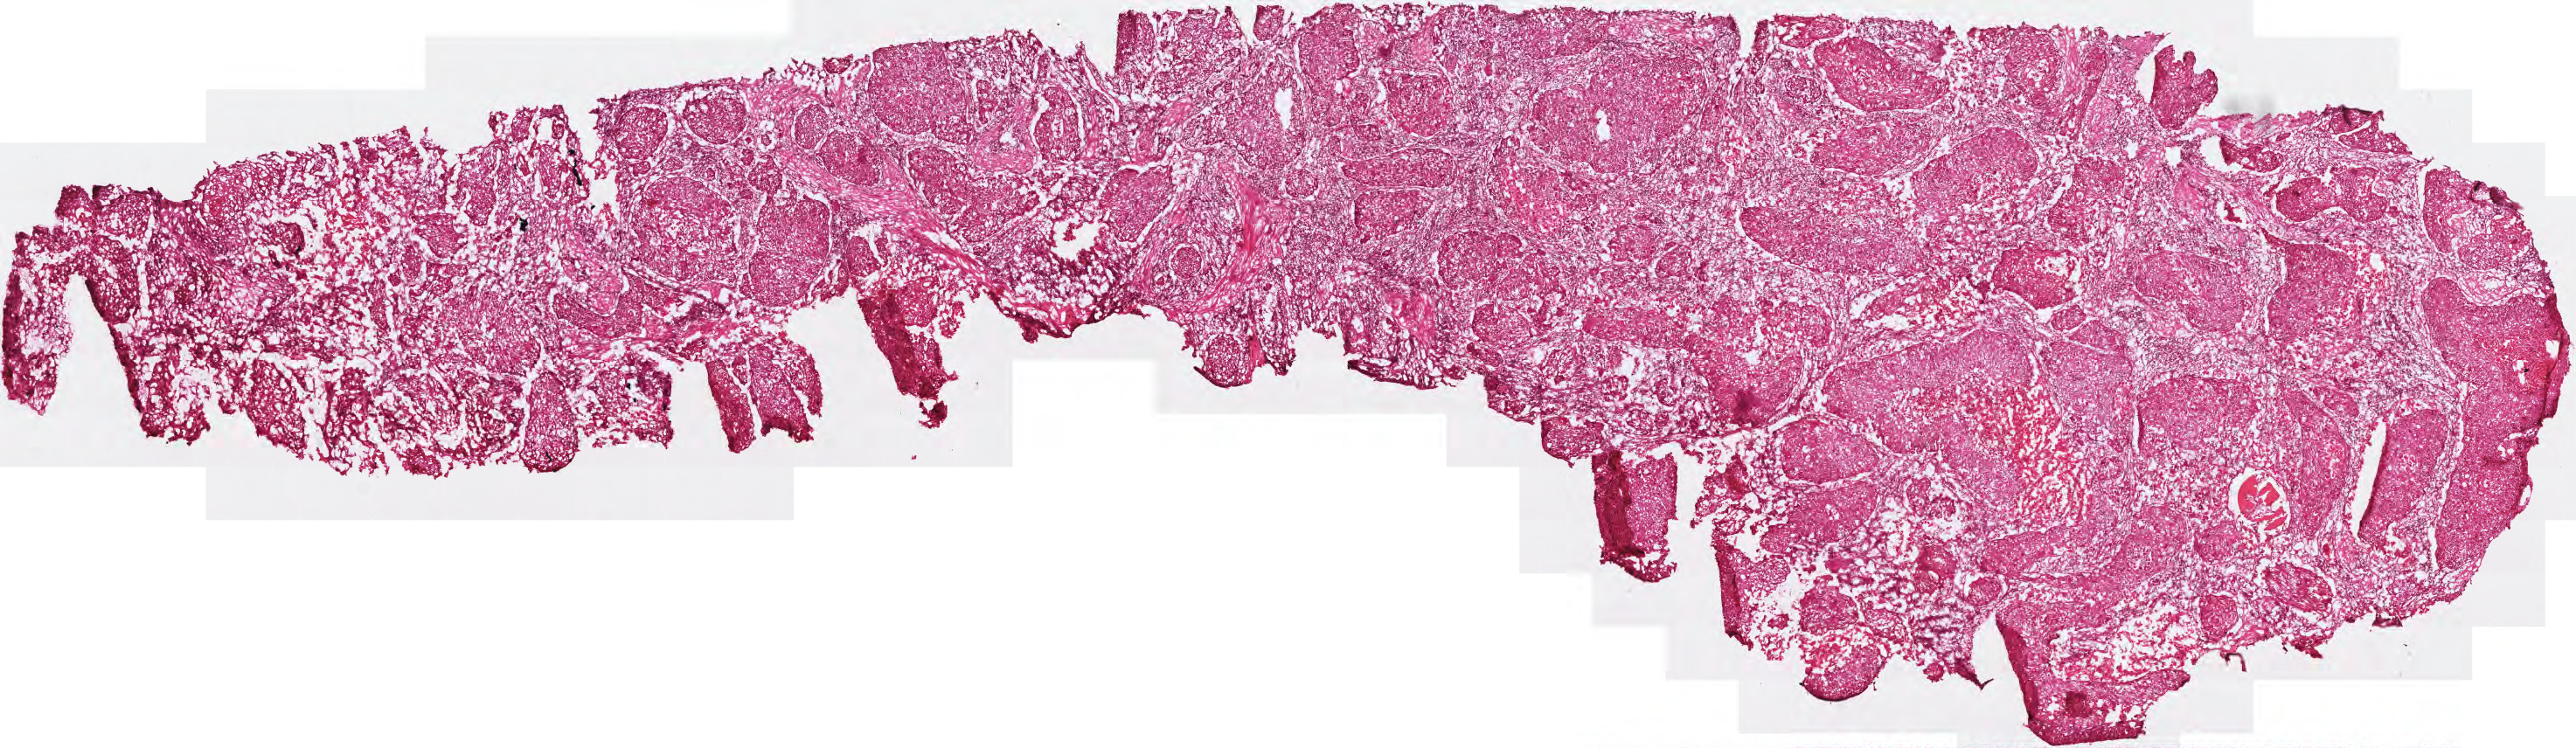
Whole-slide histology image, H&E, shown as a low-resolution overview of the whole scanned area (about 5.9 x 1.7 mm); frozen section; sample: primary tumour, head and neck. Patient: female, age at initial diagnosis 67 years. Histologic grade: G2 (moderately differentiated). Slide review estimates, as recorded: tumour cells 75%, tumour nuclei 80%, normal cells 0%, stromal cells 25%, necrosis 0%.
AJCC pathologic stage: IVA (7th edition). Histologic diagnosis: Squamous cell carcinoma, NOS (overlapping lesion of lip, oral cavity and pharynx). Lymph nodes positive (case pathology): 5 of 22 examined.